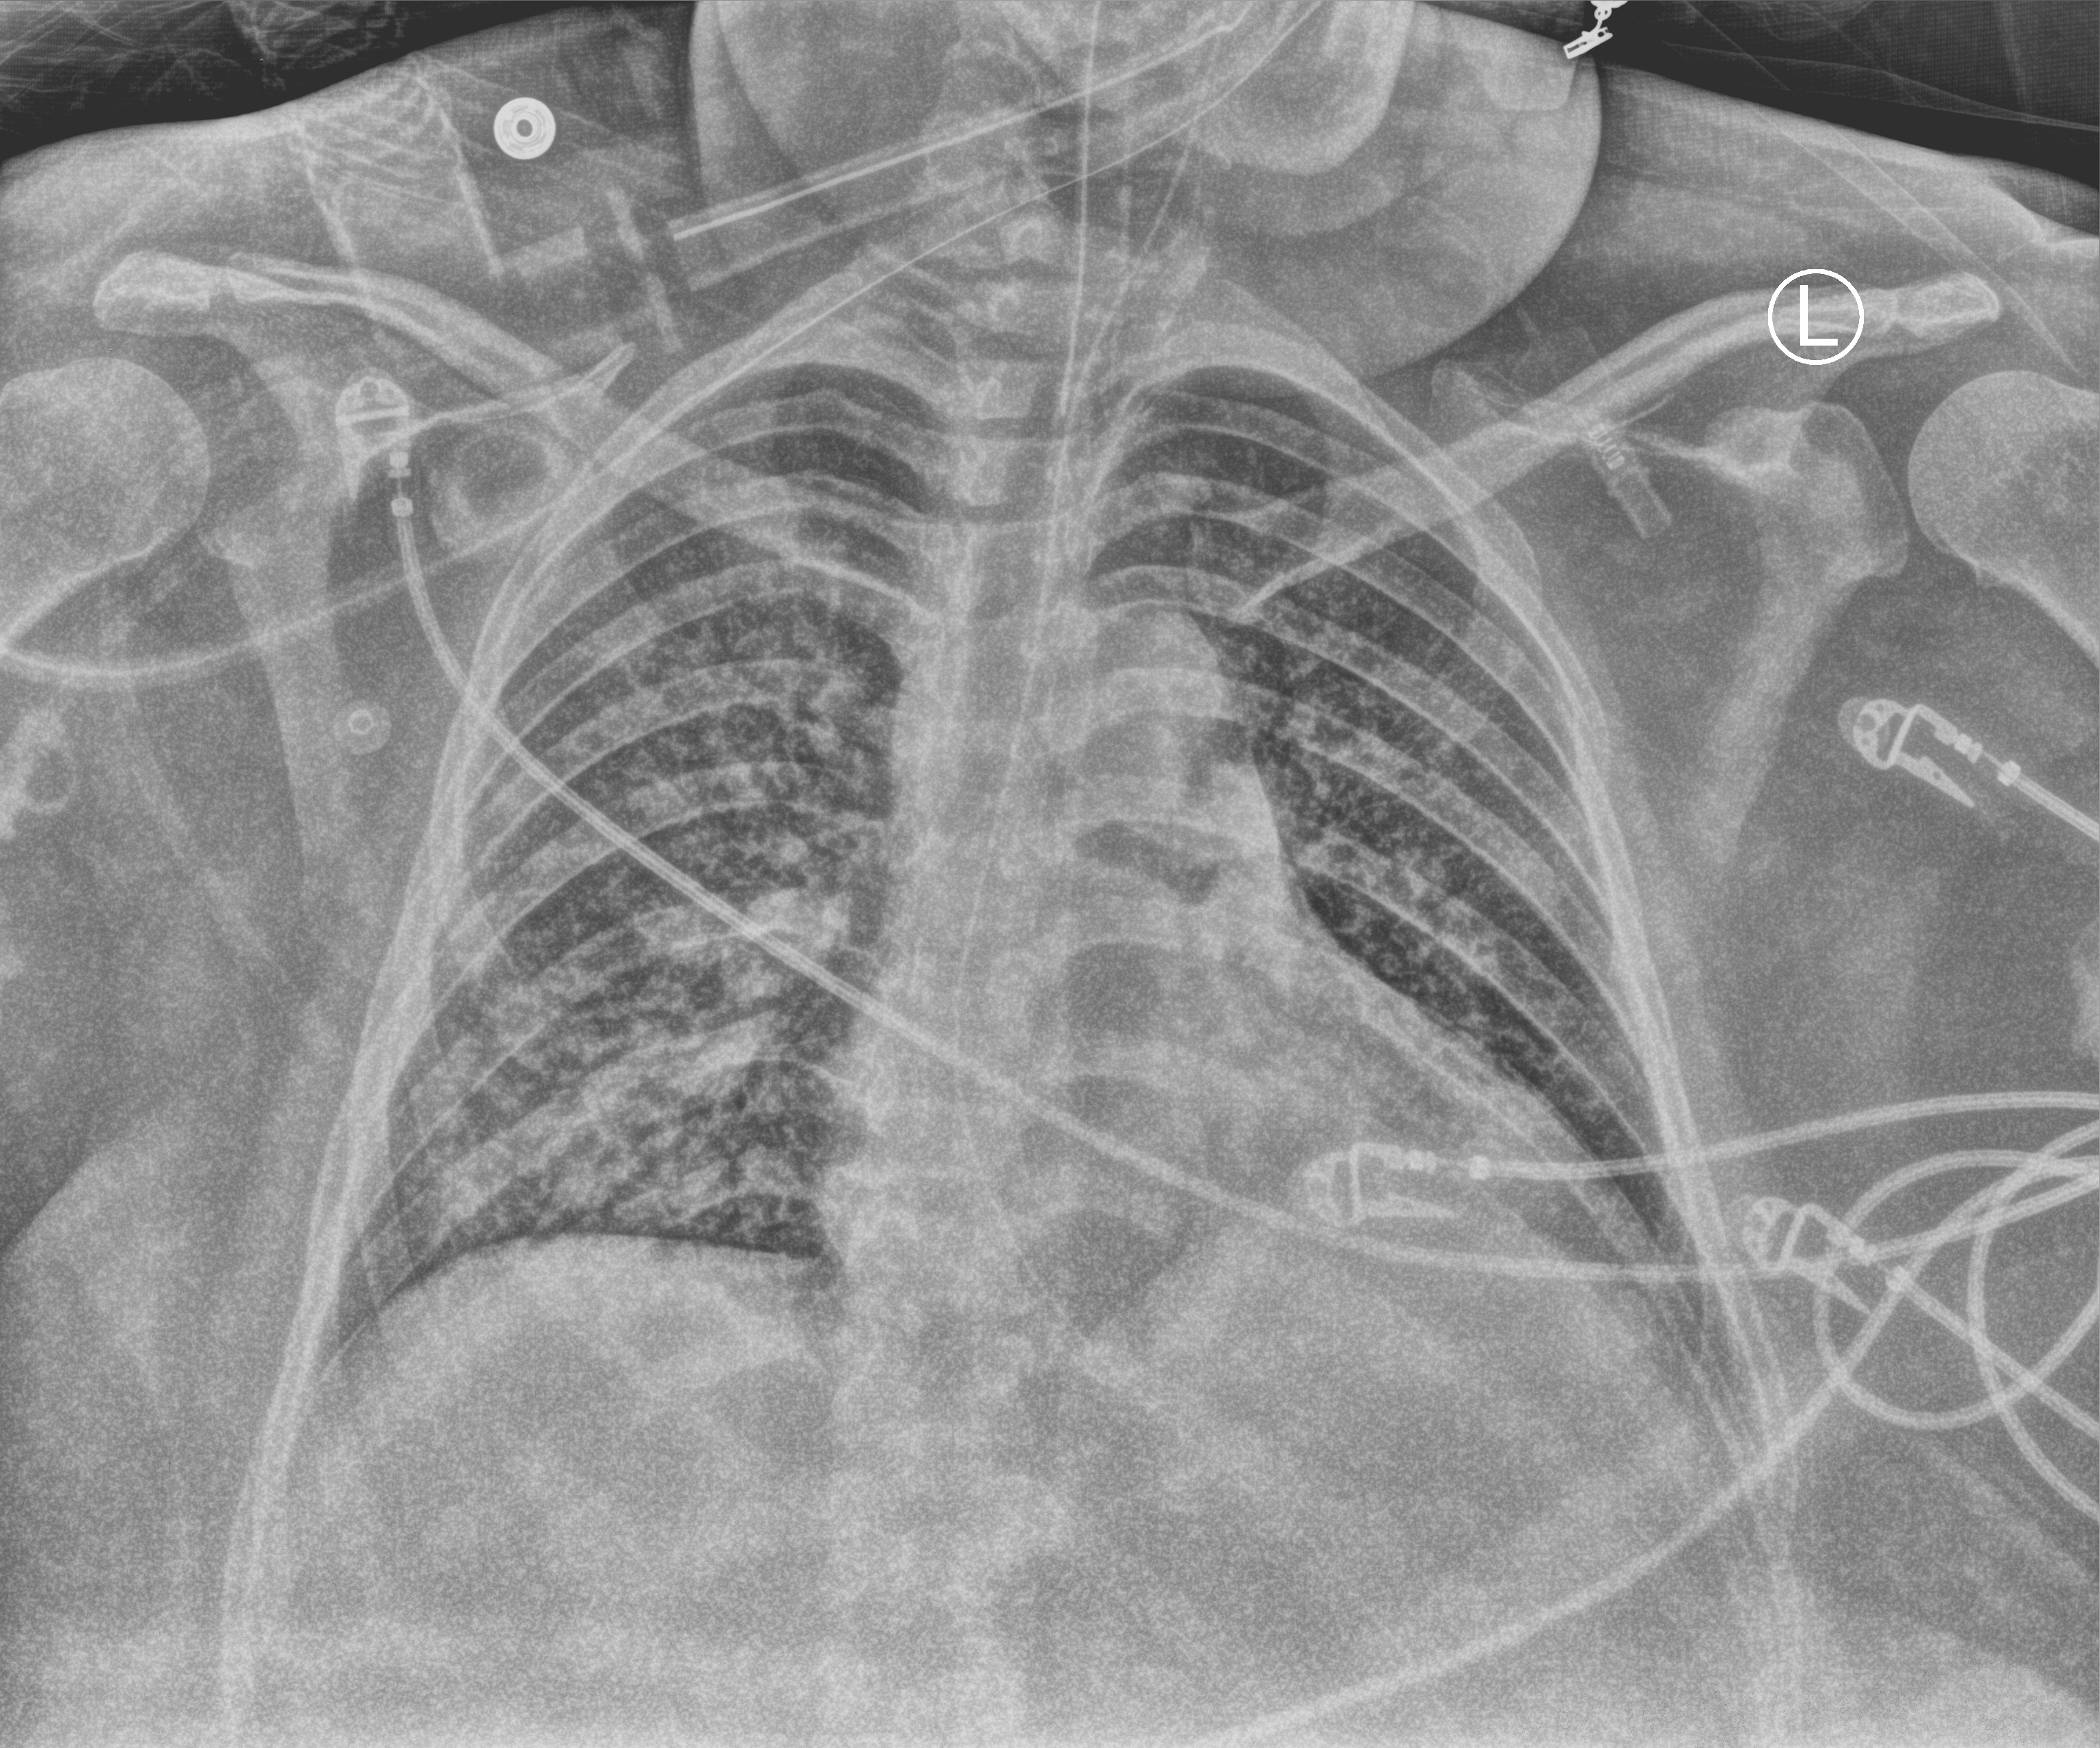
Chest X-ray (portable); anteroposterior (AP) projection. Female patient hospitalised with COVID-19, age 18–59 years.
Hospital-stay facts (about this admission, not read from this image; timing relative to this image not recorded):
- mechanically ventilated during this hospital stay: yes